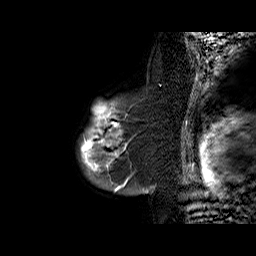
Breast MRI (dynamic contrast-enhanced), one sagittal slice. Slice 50 of 60 in the series (ordered by position). Dynamic contrast-enhanced series, time point 2 of 6 at this slice position (early post-contrast). 1.5 T. TE 6.3 ms, TR 32.4 ms. 4 mm slice thickness. 256 × 256 image matrix. Female patient. From the clinical record (not read from this slice): setting: breast cancer imaged before/during neoadjuvant chemotherapy; receptor status: triple-negative.
Outlined on this slice (semi-automatic segmentation, software-assisted and operator-edited):
- analysis volume of interest (the breast-tissue region the enhancement analysis was run in; not a lesion): box from (x=78, y=92) to (x=161, y=187) px
- tumour enhancement mask (voxels above the 100 % enhancement threshold inside the analysis volume of interest): (x=80, y=101)–(x=126, y=187)